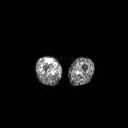
FDG PET of an extremity soft-tissue mass (from a PET/CT study), one axial slice. Slice 230 of 311 in the series (ordered by position). 3.27 mm slice thickness. 128 × 128 image matrix, field of view 700 × 700 mm. Patient: male, 56 years. Case-level facts recorded for this patient, not image findings: histological type: pleiomorphic leiomyosarcoma; grade: intermediate; site of the primary tumour: right thigh.
Outlined on this slice (expert contour drawn on MRI and transferred to this co-registered scan by the dataset authors):
- gross tumour volume including surrounding oedema: bounding box <46,59,51,63> (left, top, right, bottom; pixels)